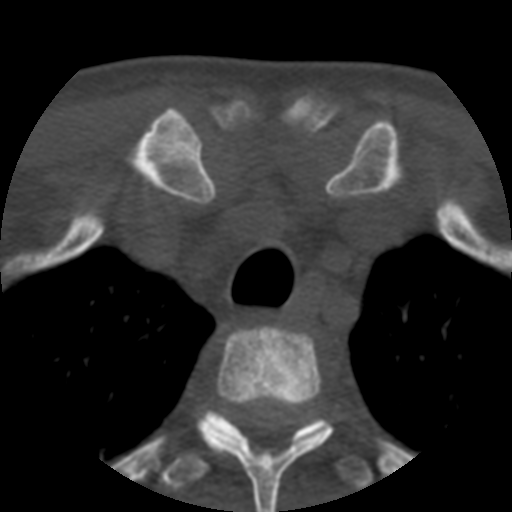
CT including the spine, one axial slice. Slice 426 of 508 in the series (ordered by position). 120 kVp. Bone window (W 1800 / L 400 HU). 1.25 mm slice thickness. 512 × 512 image matrix, field of view 160 × 160 mm. Patient age 57 years. Case-level facts recorded for this patient, not image findings: primary cancer: prostate.
Structures marked on this image (semi-automatically segmented with operator editing):
- T2 vertebra: bounding box [x1, y1, x2, y2] px = [198, 326, 332, 512]
- T3 vertebra: [161, 411, 373, 490]